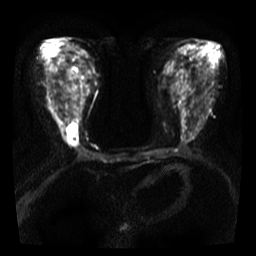
Breast MRI, one axial slice. Diffusion-weighted series; image 2 of 4 stored at this slice position (different b-values; order by instance number). 3 T. 256 × 256 image matrix, field of view 300 × 300 mm. Female patient.
Outlined on this slice (outlined manually by an expert reader):
- tumour on diffusion-weighted imaging: box from (x=66, y=124) to (x=78, y=138) px